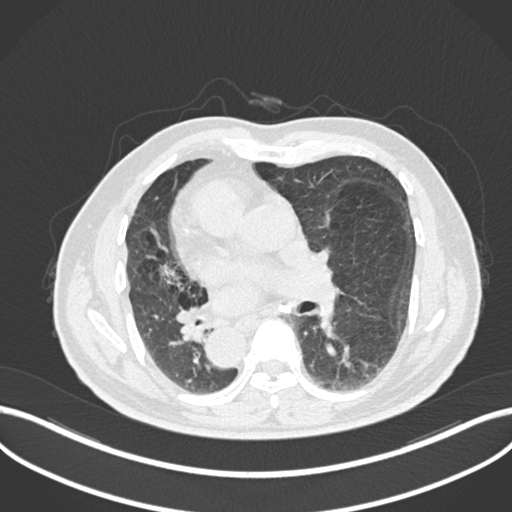
Chest CT, one axial slice; slice 110 of 206 in the series (ordered by position); reconstruction kernel B30f; 120 kVp; lung window (W 1500 / L -600 HU); 1 mm slice thickness; 512 × 512 image matrix. Male patient, age 67 years. Case-level facts recorded for this patient, not image findings: clinical TNM (as recorded): T2a N0 M0.
Structures marked on this image (bounding box drawn by a radiologist):
- lung tumour (recorded histology: squamous cell carcinoma): box from (x=172, y=305) to (x=212, y=345) px